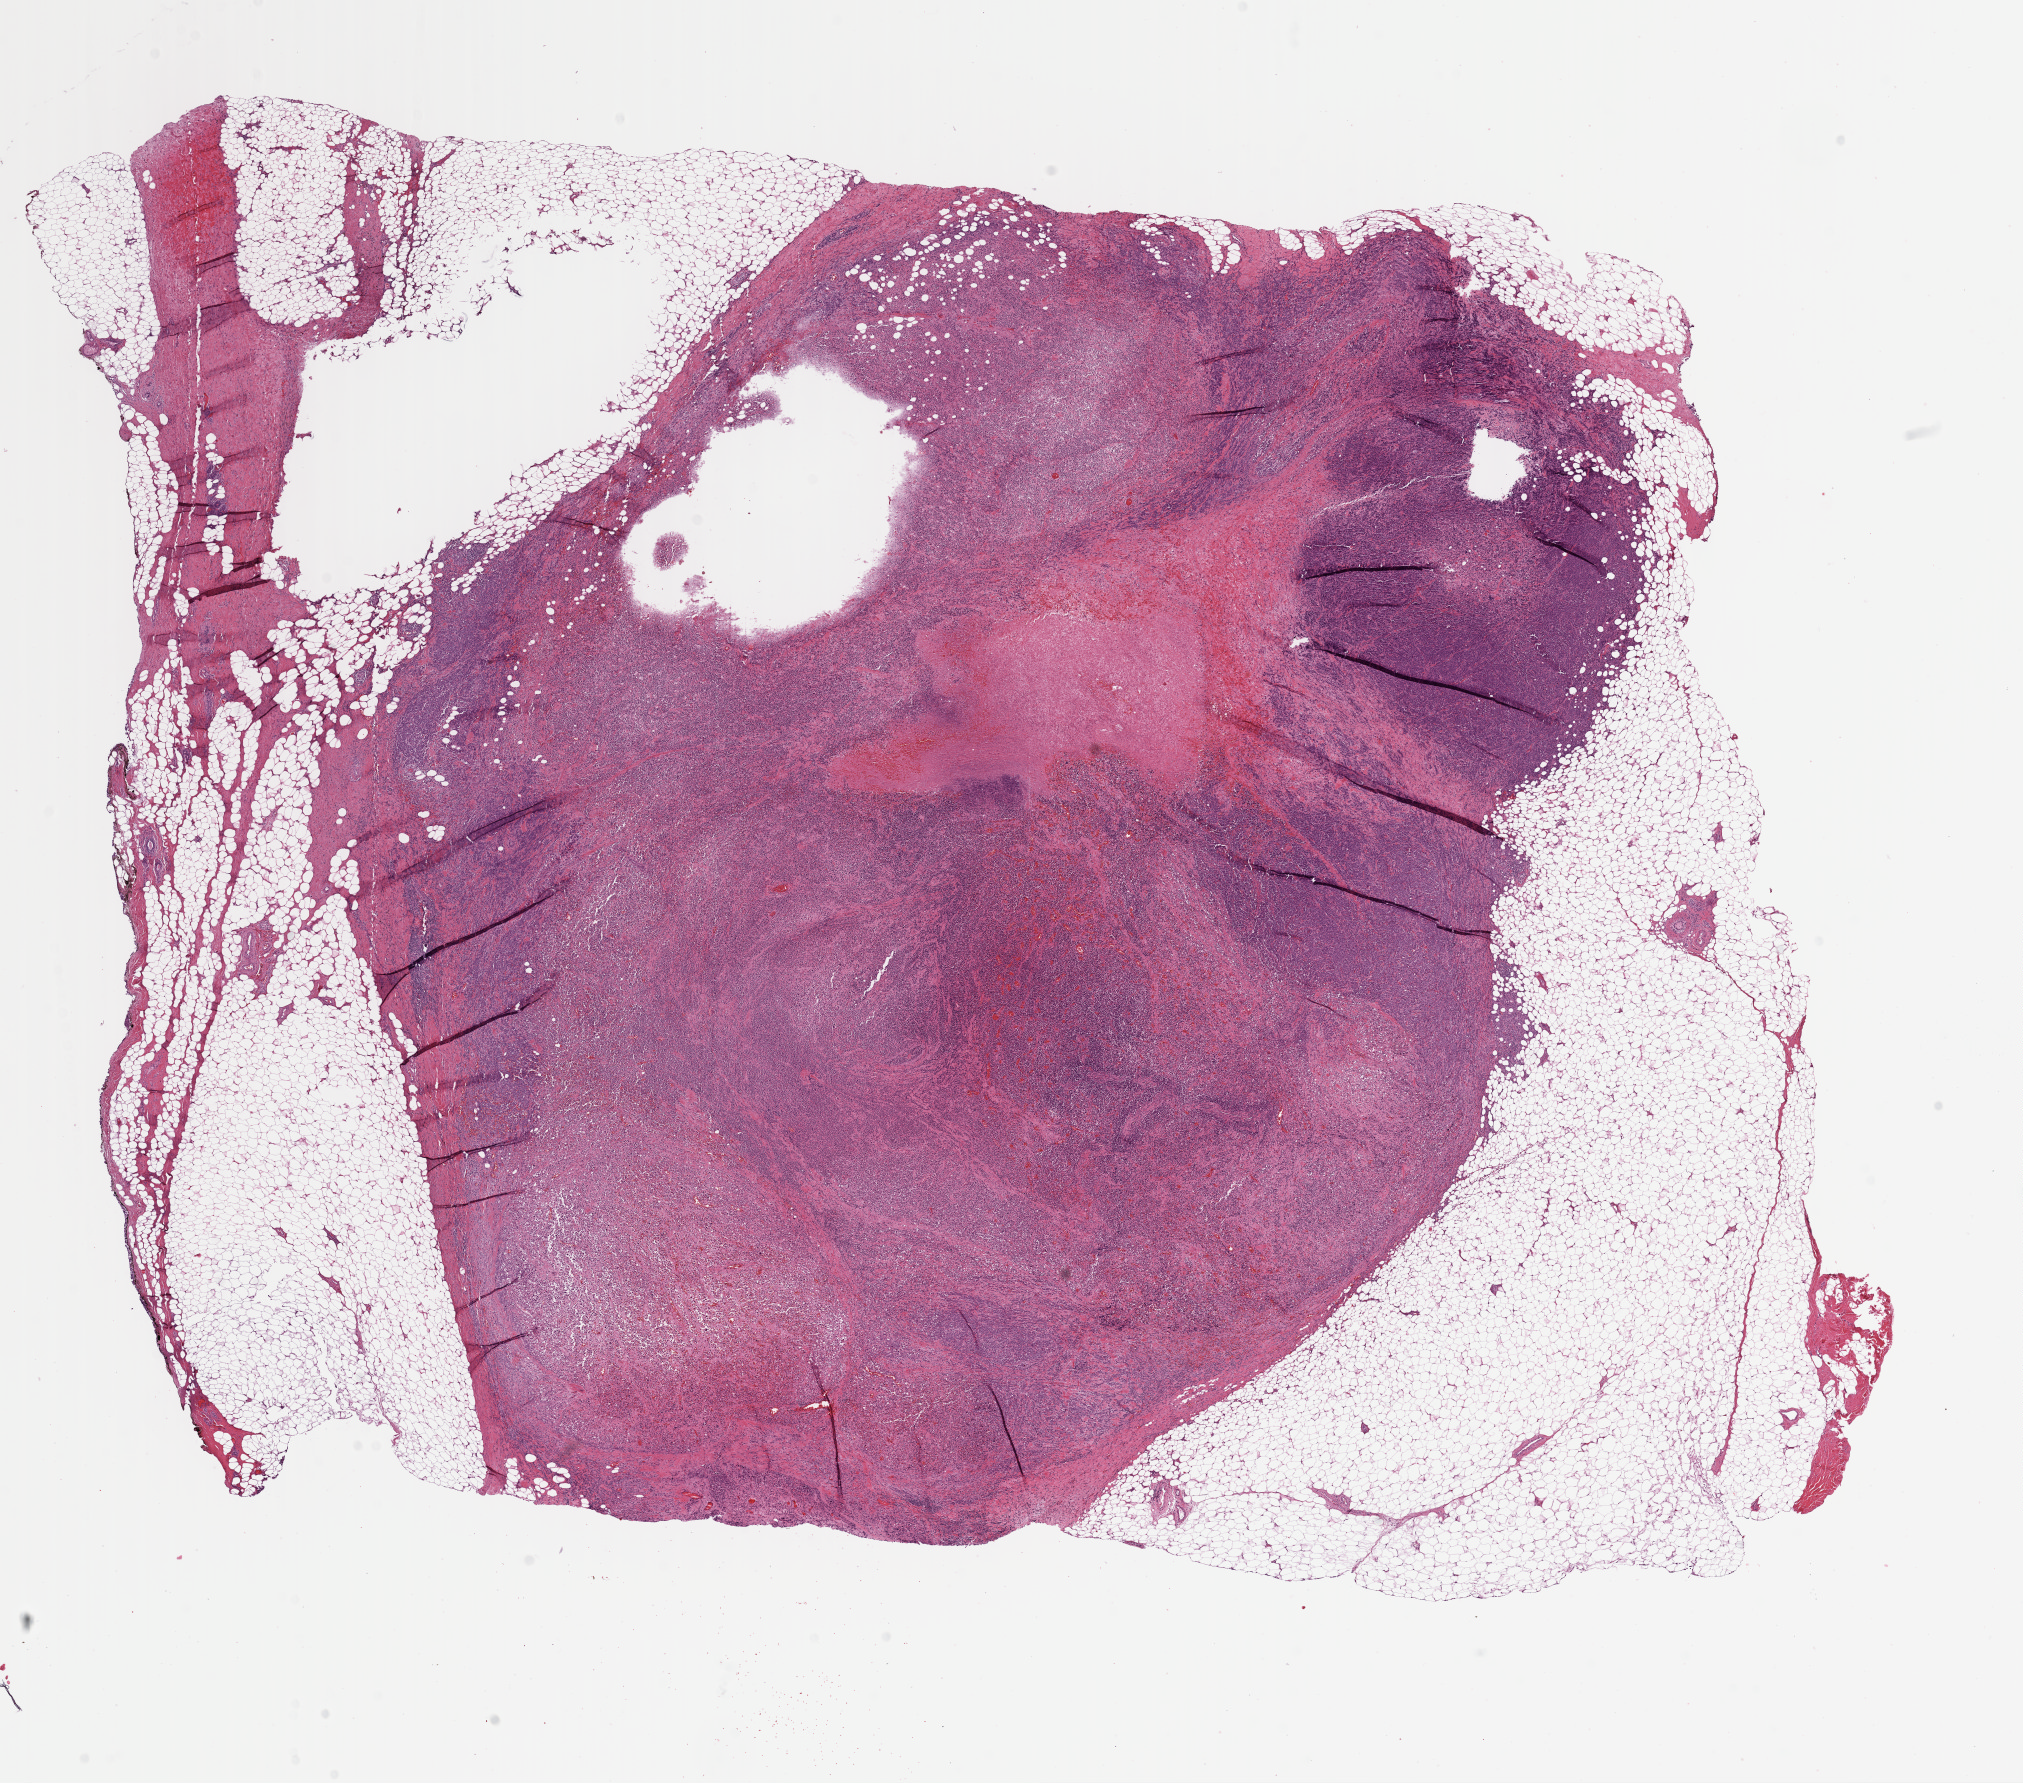
Digitized Hematoxylin and eosin (H&E) stained tissue section (whole slide), whole scanned area (about 16.0 x 14.1 mm) shown as a low-resolution overview; formalin-fixed paraffin-embedded (FFPE) diagnostic section; breast, primary tumour sample. Patient: female, age at initial diagnosis 50 years.
• AJCC pathologic stage: IIIA
• lymph nodes positive (case pathology): 5 of 14 examined
• histologic diagnosis: Infiltrating duct carcinoma, NOS